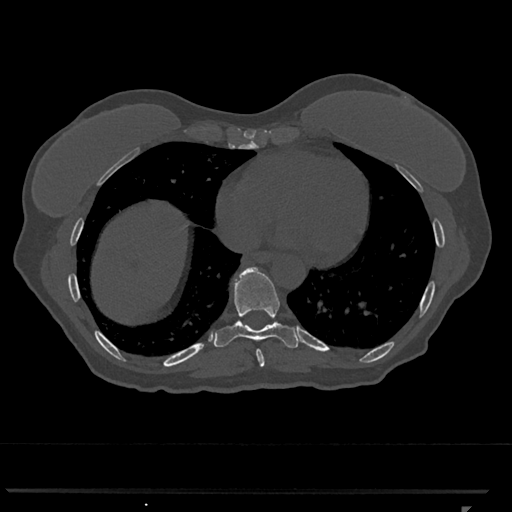
CT including the spine, one axial slice. Slice 621 of 793 in the series (ordered by position). Reconstruction kernel Br40s/3. 120 kVp. Bone window (W 1800 / L 400 HU). 0.5 mm slice thickness. 512 × 512 image matrix, field of view 380 × 380 mm. Patient: female, 62 years. Case-level facts recorded for this patient, not image findings: primary cancer: renal.
Structures marked on this image (semi-automatic segmentation, software-assisted and operator-edited):
- T8 vertebra: bounding box [x1, y1, x2, y2] px = [256, 349, 265, 367]
- T9 vertebra: [214, 267, 299, 348]